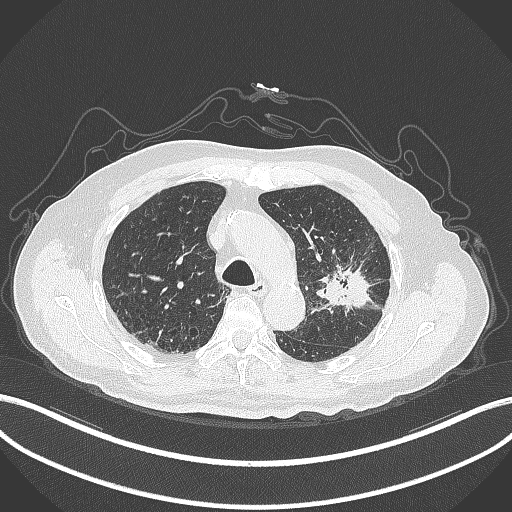
Chest CT, one axial slice. Position 212 of 331 along the scan axis. 120 kVp. Lung window (W 1500 / L -600 HU). 512 × 512 image matrix, field of view 400 × 400 mm. Patient: male, 79 years. From the clinical record (not read from this slice): clinical TNM (as recorded): T2a N1 M1; histopathological grade: G3.
Structures marked on this image (rectangle marked by the reading radiologist):
- lung tumour (recorded histology: adenocarcinoma): bounding box (x1, y1, x2, y2) in pixels: (305, 250, 382, 317)